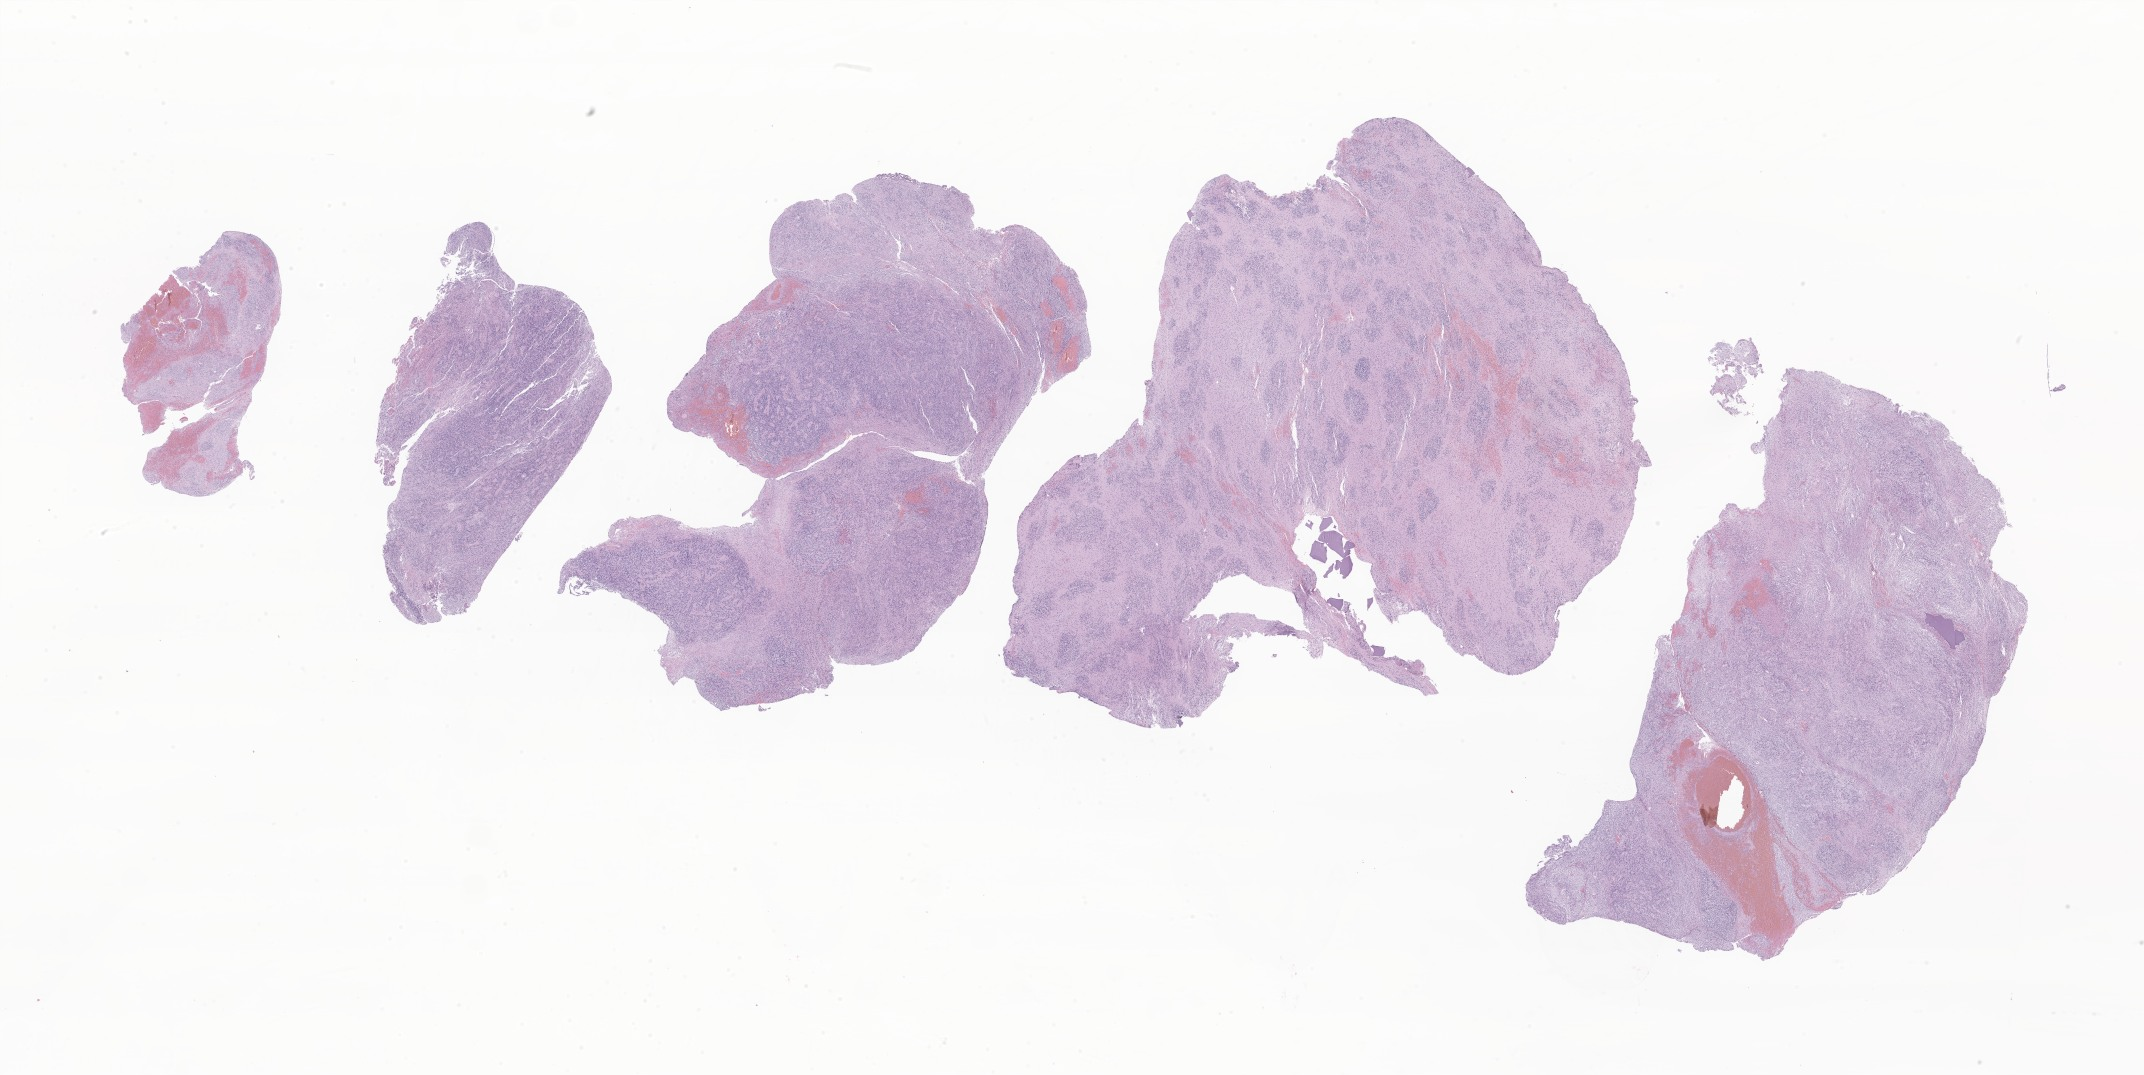
Digitized H&E-stained section of tumor tissue from the cerebral ventricle — shown as a low-resolution overview of the whole scanned area (about 36.2 x 18.1 mm), FFPE section. Patient male; age 64 months (5 years 4 months).
Recorded diagnosis: Ependymoma, NOS.